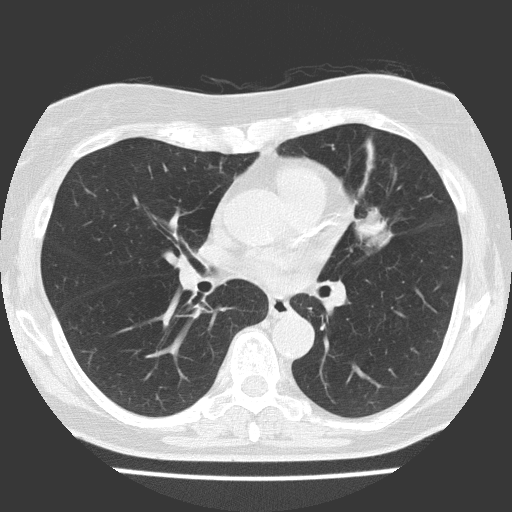
Low-dose screening chest CT, axial slice; baseline screening round; lung window (W 1500 / L -600 HU); lung (sharp) reconstruction kernel (FC51); slice 74 of 151 in the series; 512 × 512 image matrix, field of view 309 × 309 mm. Female, age 70 years at enrolment. Current smoker at enrolment.
Expert reader's lesion annotation, box from (x=320, y=177) to (x=431, y=272) px. The screening reader recorded 2 non-calcified nodules or masses ≥4 mm on this exam (left upper lobe, right upper lobe); which of them this box marks is not recorded.